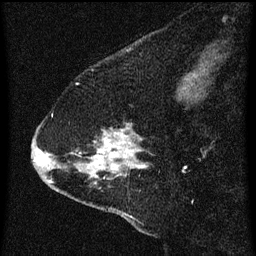
Breast MRI (dynamic contrast-enhanced), one sagittal slice. Slice 15 of 60 in the series (ordered by position). Dynamic contrast-enhanced series, image 2 of 3 at this slice position (ordered by acquisition). 1.5 T. TE 4.2 ms, TR 8 ms. 256 × 256 image matrix, field of view 180 × 180 mm. Patient: female, 47 years.
Outlined on this slice (semi-automatically segmented with operator editing):
- analysis volume of interest (the breast-tissue region the enhancement analysis was run in; not a lesion): bounding box (x1, y1, x2, y2) in pixels: (36, 114, 153, 213)
- tumour enhancement mask (voxels above the 70 % enhancement threshold inside the analysis volume of interest): (48, 132, 145, 183)